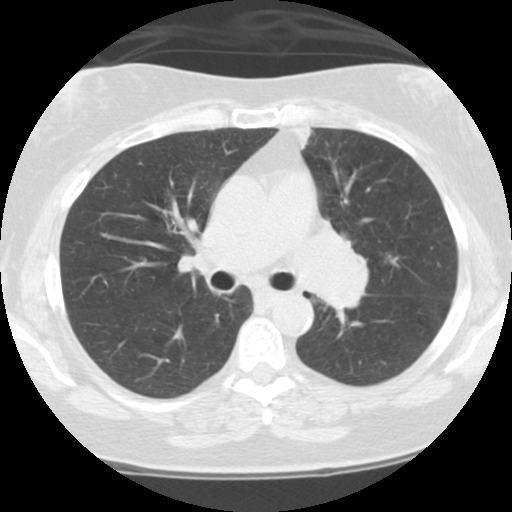
Low-dose screening chest CT, one axial slice; slice 67 of 108 in the series (ordered by position); 120 kVp; lung window (W 1500 / L -600 HU); 2.5 mm slice thickness; 512 × 512 image matrix.
Outlined on this slice (outlined manually by an expert reader):
- lesion 1 (tumor, hilum of left lung): box from (x=297, y=230) to (x=368, y=319) px